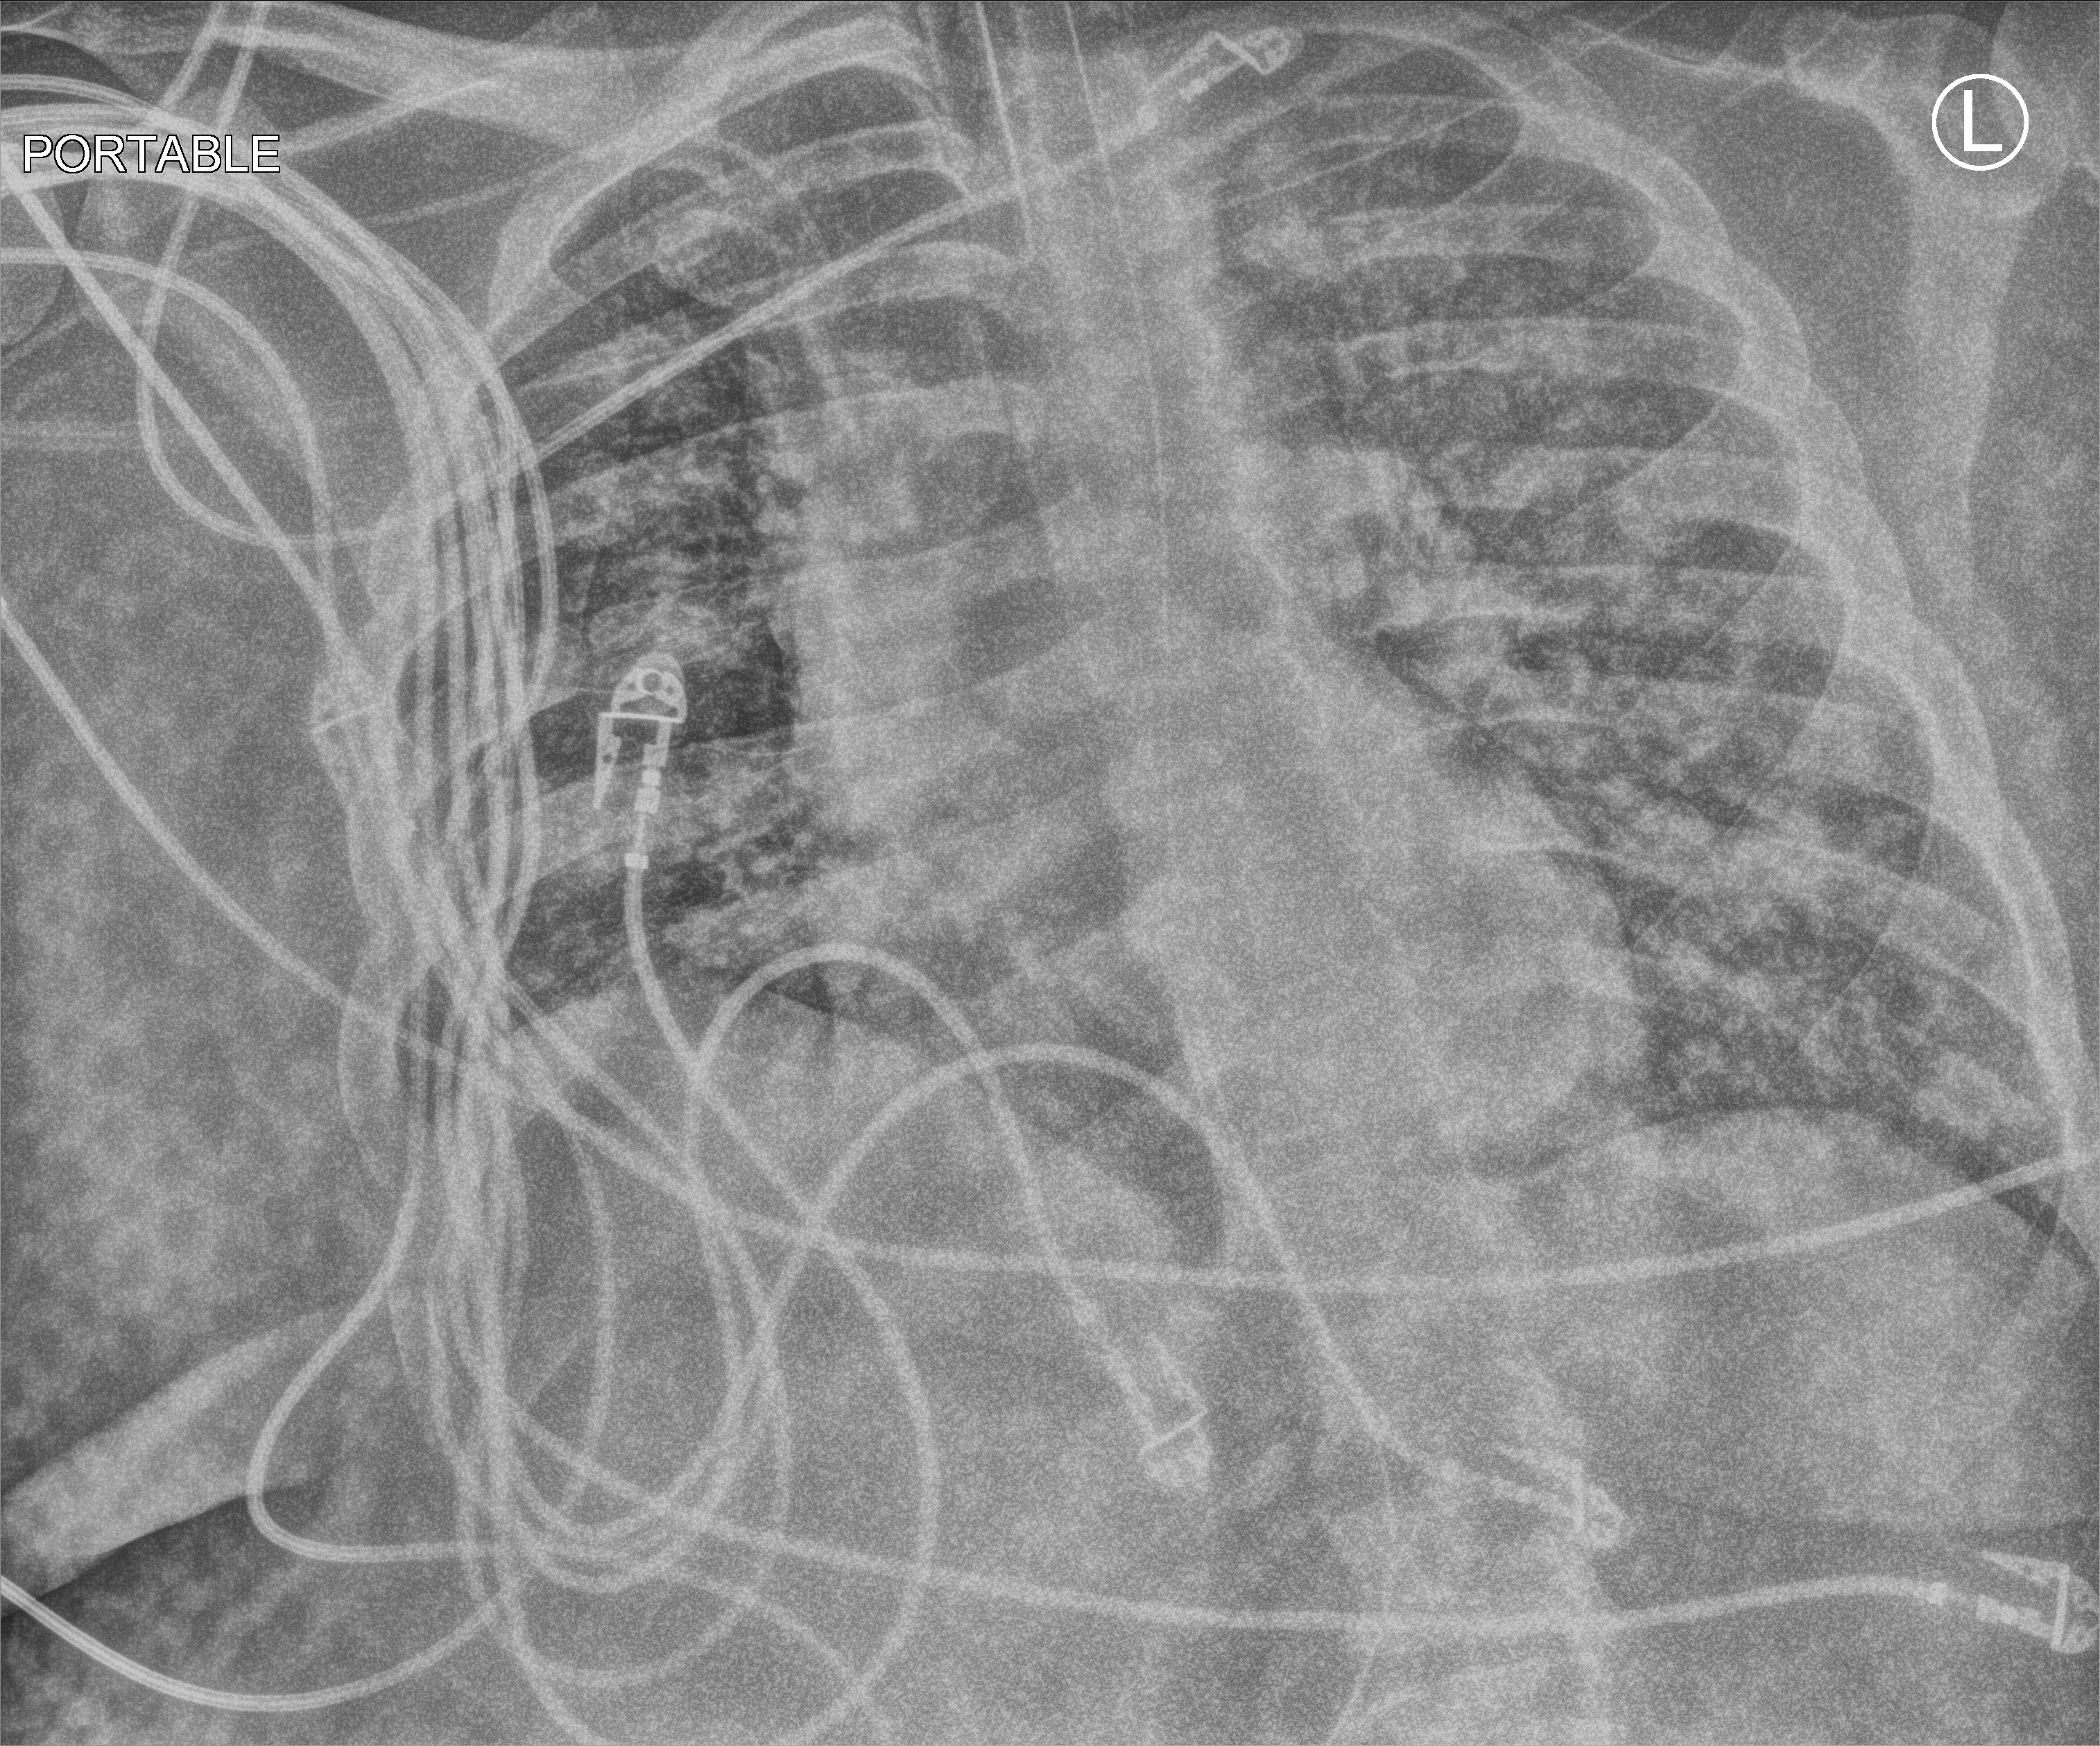
Portable chest radiograph, anteroposterior (AP) projection. Patient hospitalised with COVID-19, aged 18–59 years.
Hospital-stay facts (about this admission, not read from this image; timing relative to this image not recorded): mechanically ventilated during this hospital stay: yes; diabetes (admission record): yes.